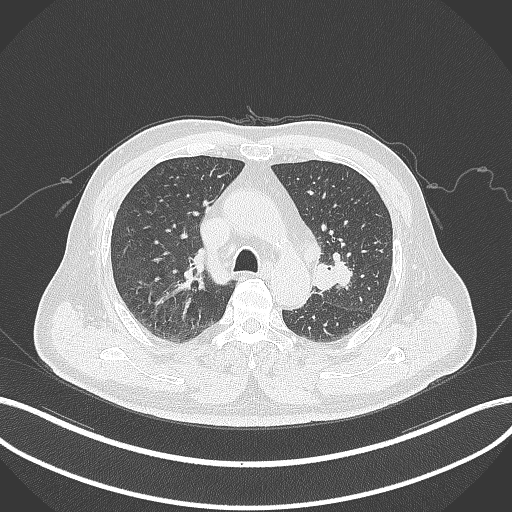
Chest CT, one axial slice. Position 206 of 286 along the scan axis. Reconstruction kernel B70f. 120 kVp. Lung window (W 1500 / L -600 HU). 1 mm slice thickness. 512 × 512 image matrix, field of view 400 × 400 mm. Male patient, age 67 years. From the clinical record (not read from this slice): clinical TNM (as recorded): T2a N1 M0.
Outlined on this slice (bounding box drawn by a radiologist):
- lung tumour (recorded histology: adenocarcinoma): box from (x=308, y=257) to (x=358, y=294) px